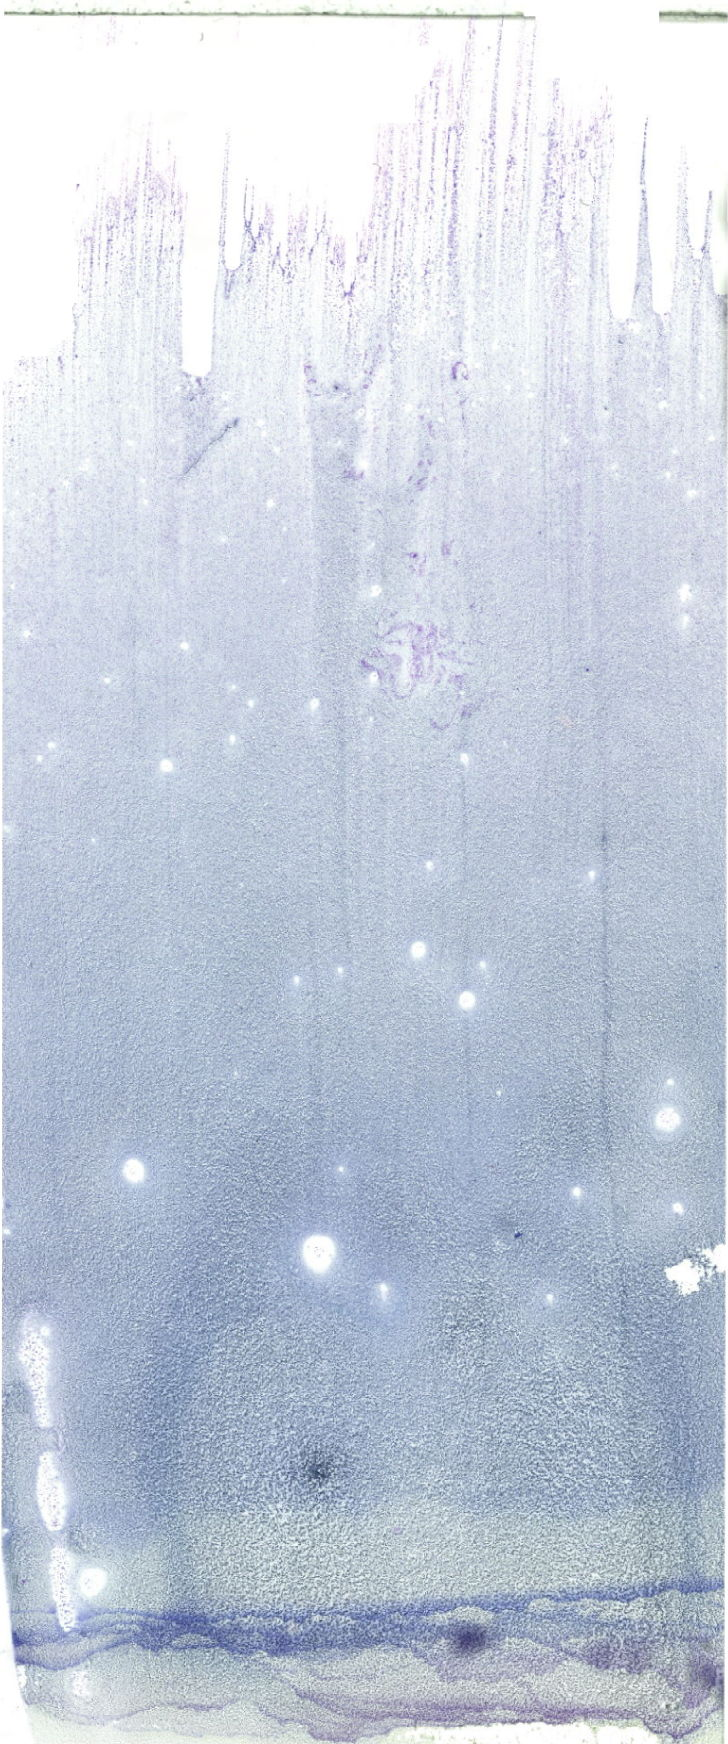
May-Grünwald-Giemsa (MGG)-stained marrow aspirate smear (whole slide) — shown as a low-resolution overview of the whole scanned area (about 20.6 x 49.4 mm). Female patient.
Diagnosis: T Acute Lymphoblastic Leukemia.